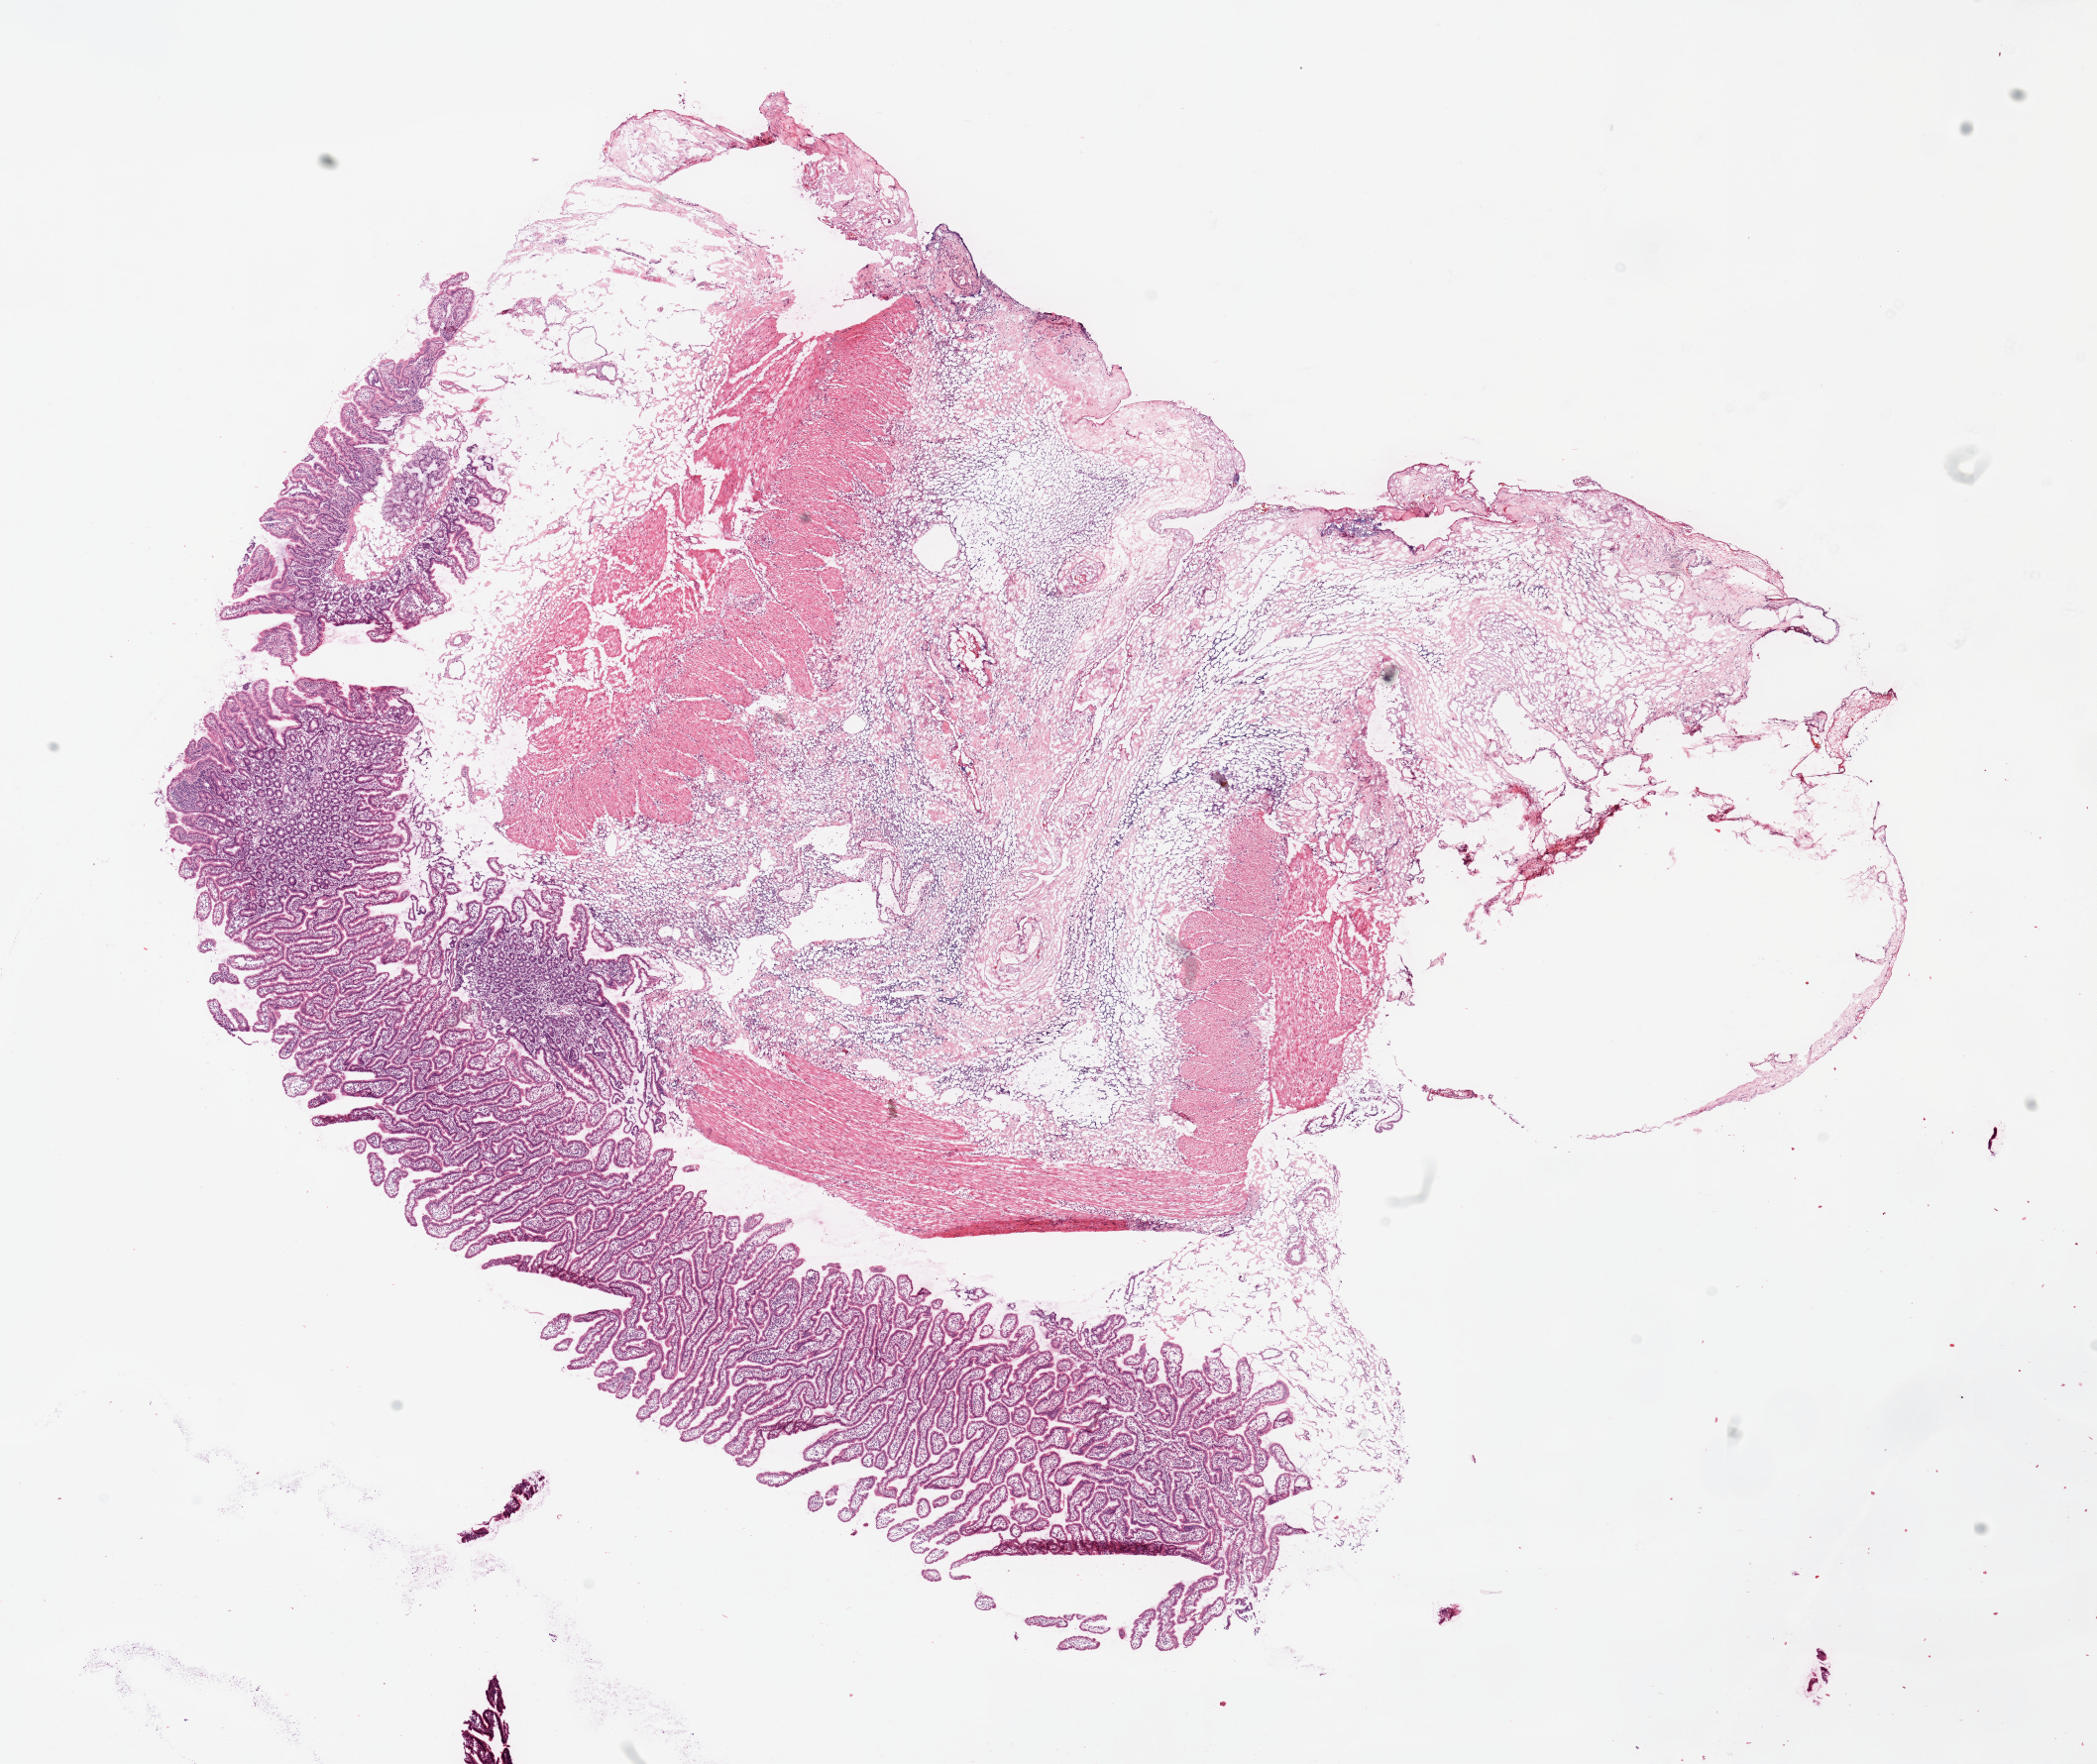
Digitized Hematoxylin and eosin (H&E) stained tissue section (whole slide) — shown as a low-resolution overview of the whole scanned area (about 16.7 x 14.1 mm), pancreas, normal (non-tumour) tissue. Patient: male, age 69 years.
This section: normal (non-tumour) tissue from the same patient. Patient diagnosis: Infiltrating duct carcinoma, NOS.